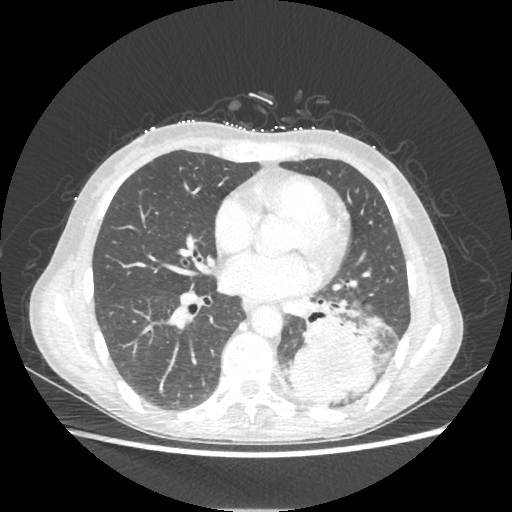
Chest CT, one axial slice. Position 102 of 221 along the scan axis. Reconstruction kernel STANDARD. Lung window (W 1500 / L -600 HU). 1.25 mm slice thickness. 512 × 512 image matrix, field of view 360 × 360 mm. Female patient, age 53 years. From the clinical record (not read from this slice): clinical TNM (as recorded): T3 N0 M0.
Annotated regions visible in this slice (rectangle marked by the reading radiologist):
- lung tumour (recorded histology: adenocarcinoma): box from (x=285, y=318) to (x=376, y=403) px